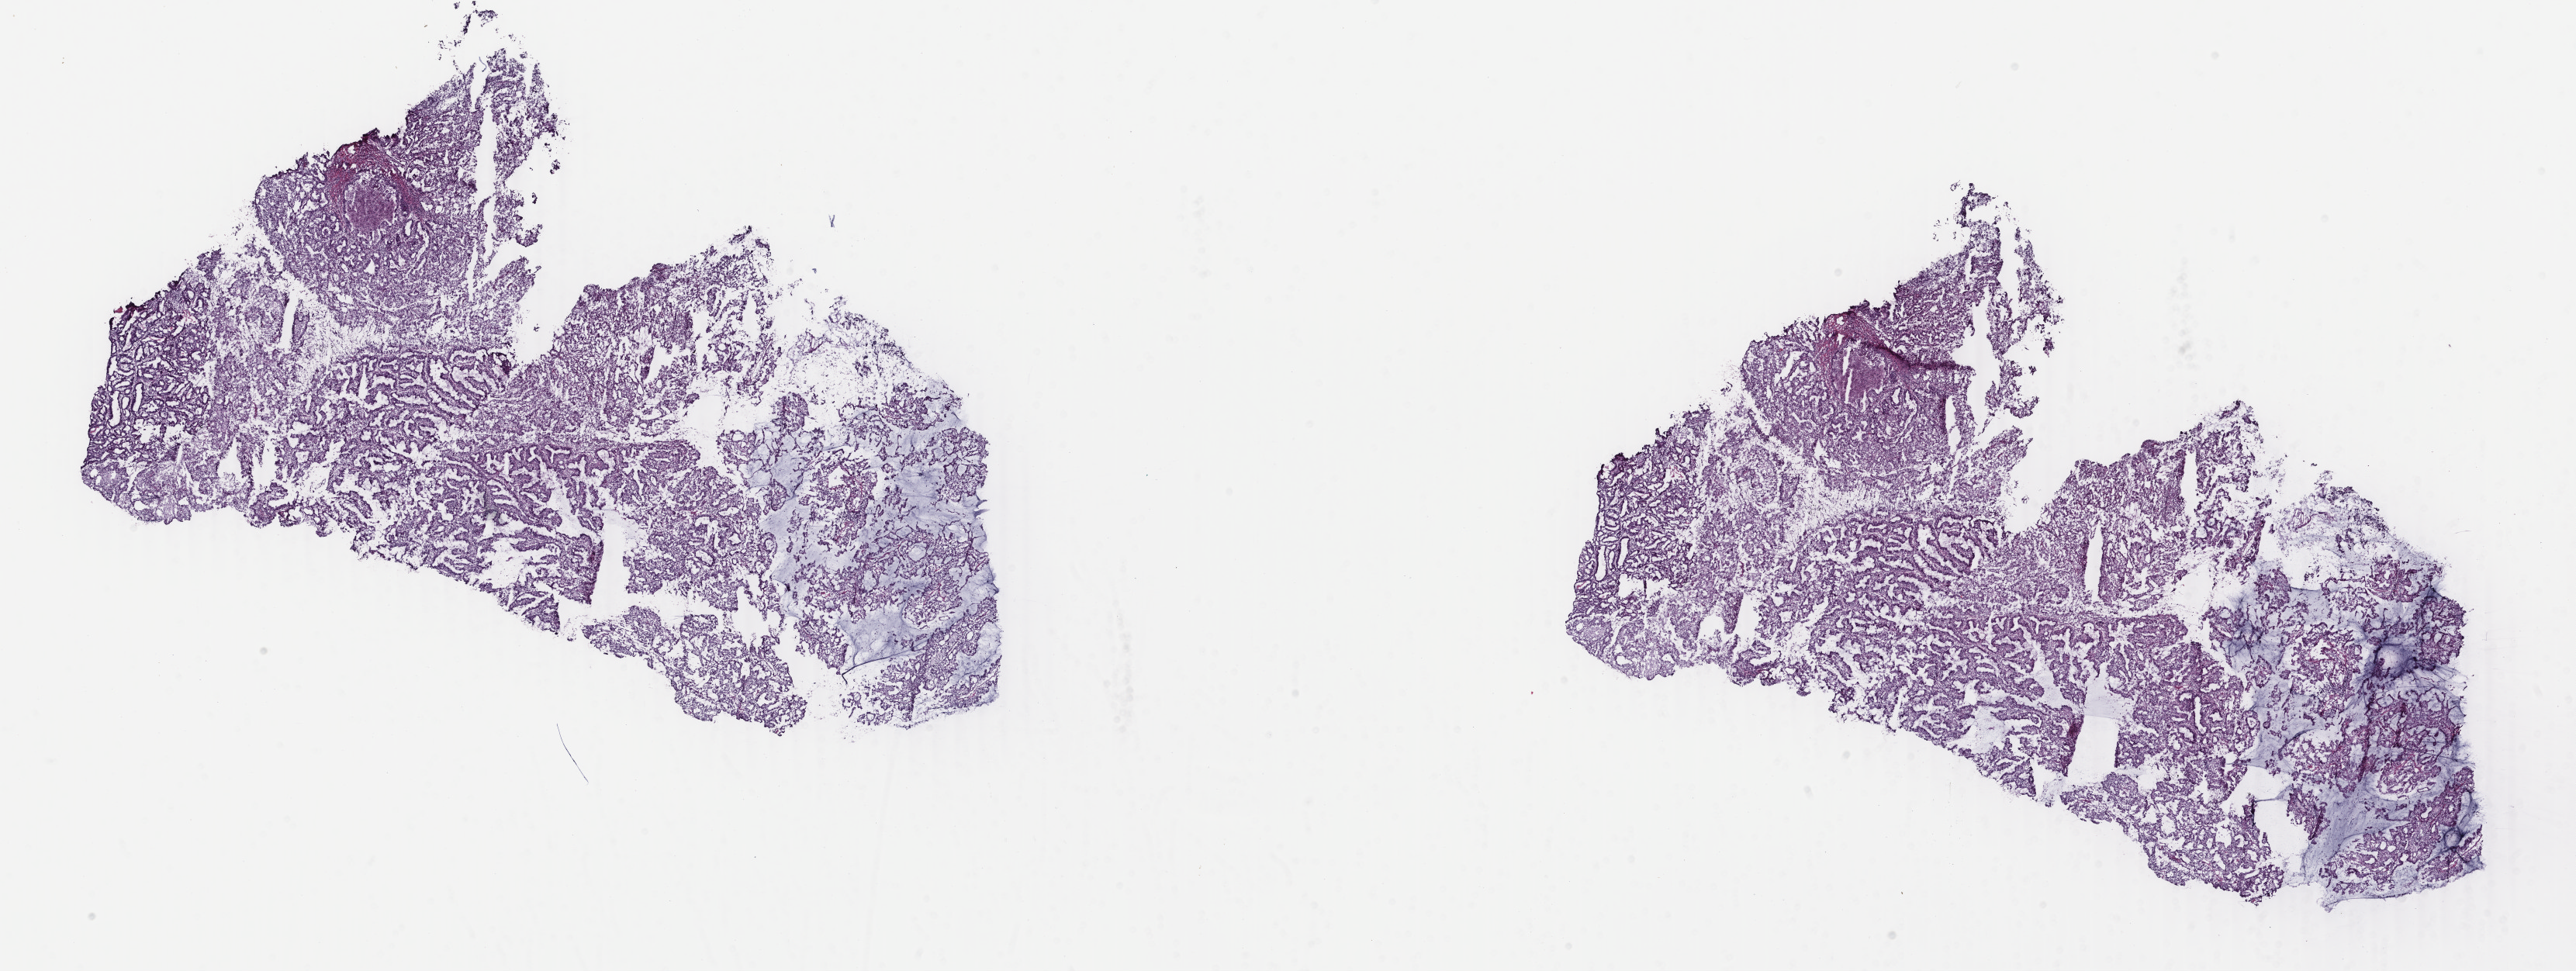
Digitized H&E-stained tissue section (whole slide), whole scanned area (about 26.4 x 10.0 mm, acquisition: 40x scan) shown as a low-resolution overview. Frozen section from the bottom of the tissue portion. Primary tumour sample from the uterus. Female patient; age at initial diagnosis 59 years. Histologic grade: G1 (well differentiated). Pathologist review of this section (percent, as recorded): tumour cells 100%, tumour nuclei 70%, normal cells 0%, stromal cells 0%, necrosis 0%. Inflammatory infiltration, as recorded: lymphocyte infiltration 0%, monocyte infiltration 0%, neutrophil infiltration 0%.
Pathologic diagnosis: Endometrioid adenocarcinoma, secretory variant (endometrium). FIGO stage: IB.